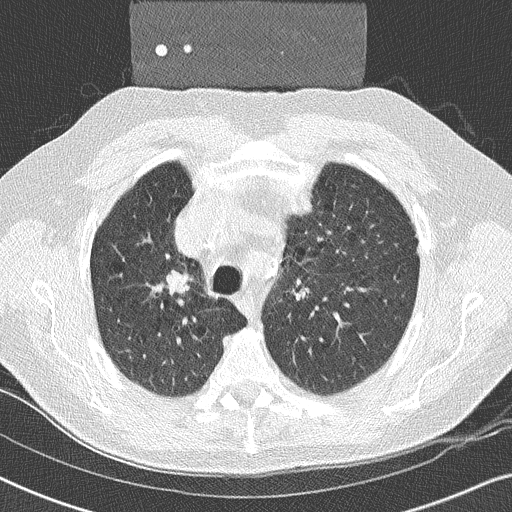
Low-dose screening chest CT, one axial slice. Reconstruction kernel B50f. 120 kVp. Lung window (W 1500 / L -600 HU). 2 mm slice thickness. 512 × 512 image matrix.
Annotated regions visible in this slice (expert manual segmentation):
- lesion 1 (tumor, upper lobe of right lung): bounding box (x1, y1, x2, y2) in pixels: (167, 270, 186, 292)